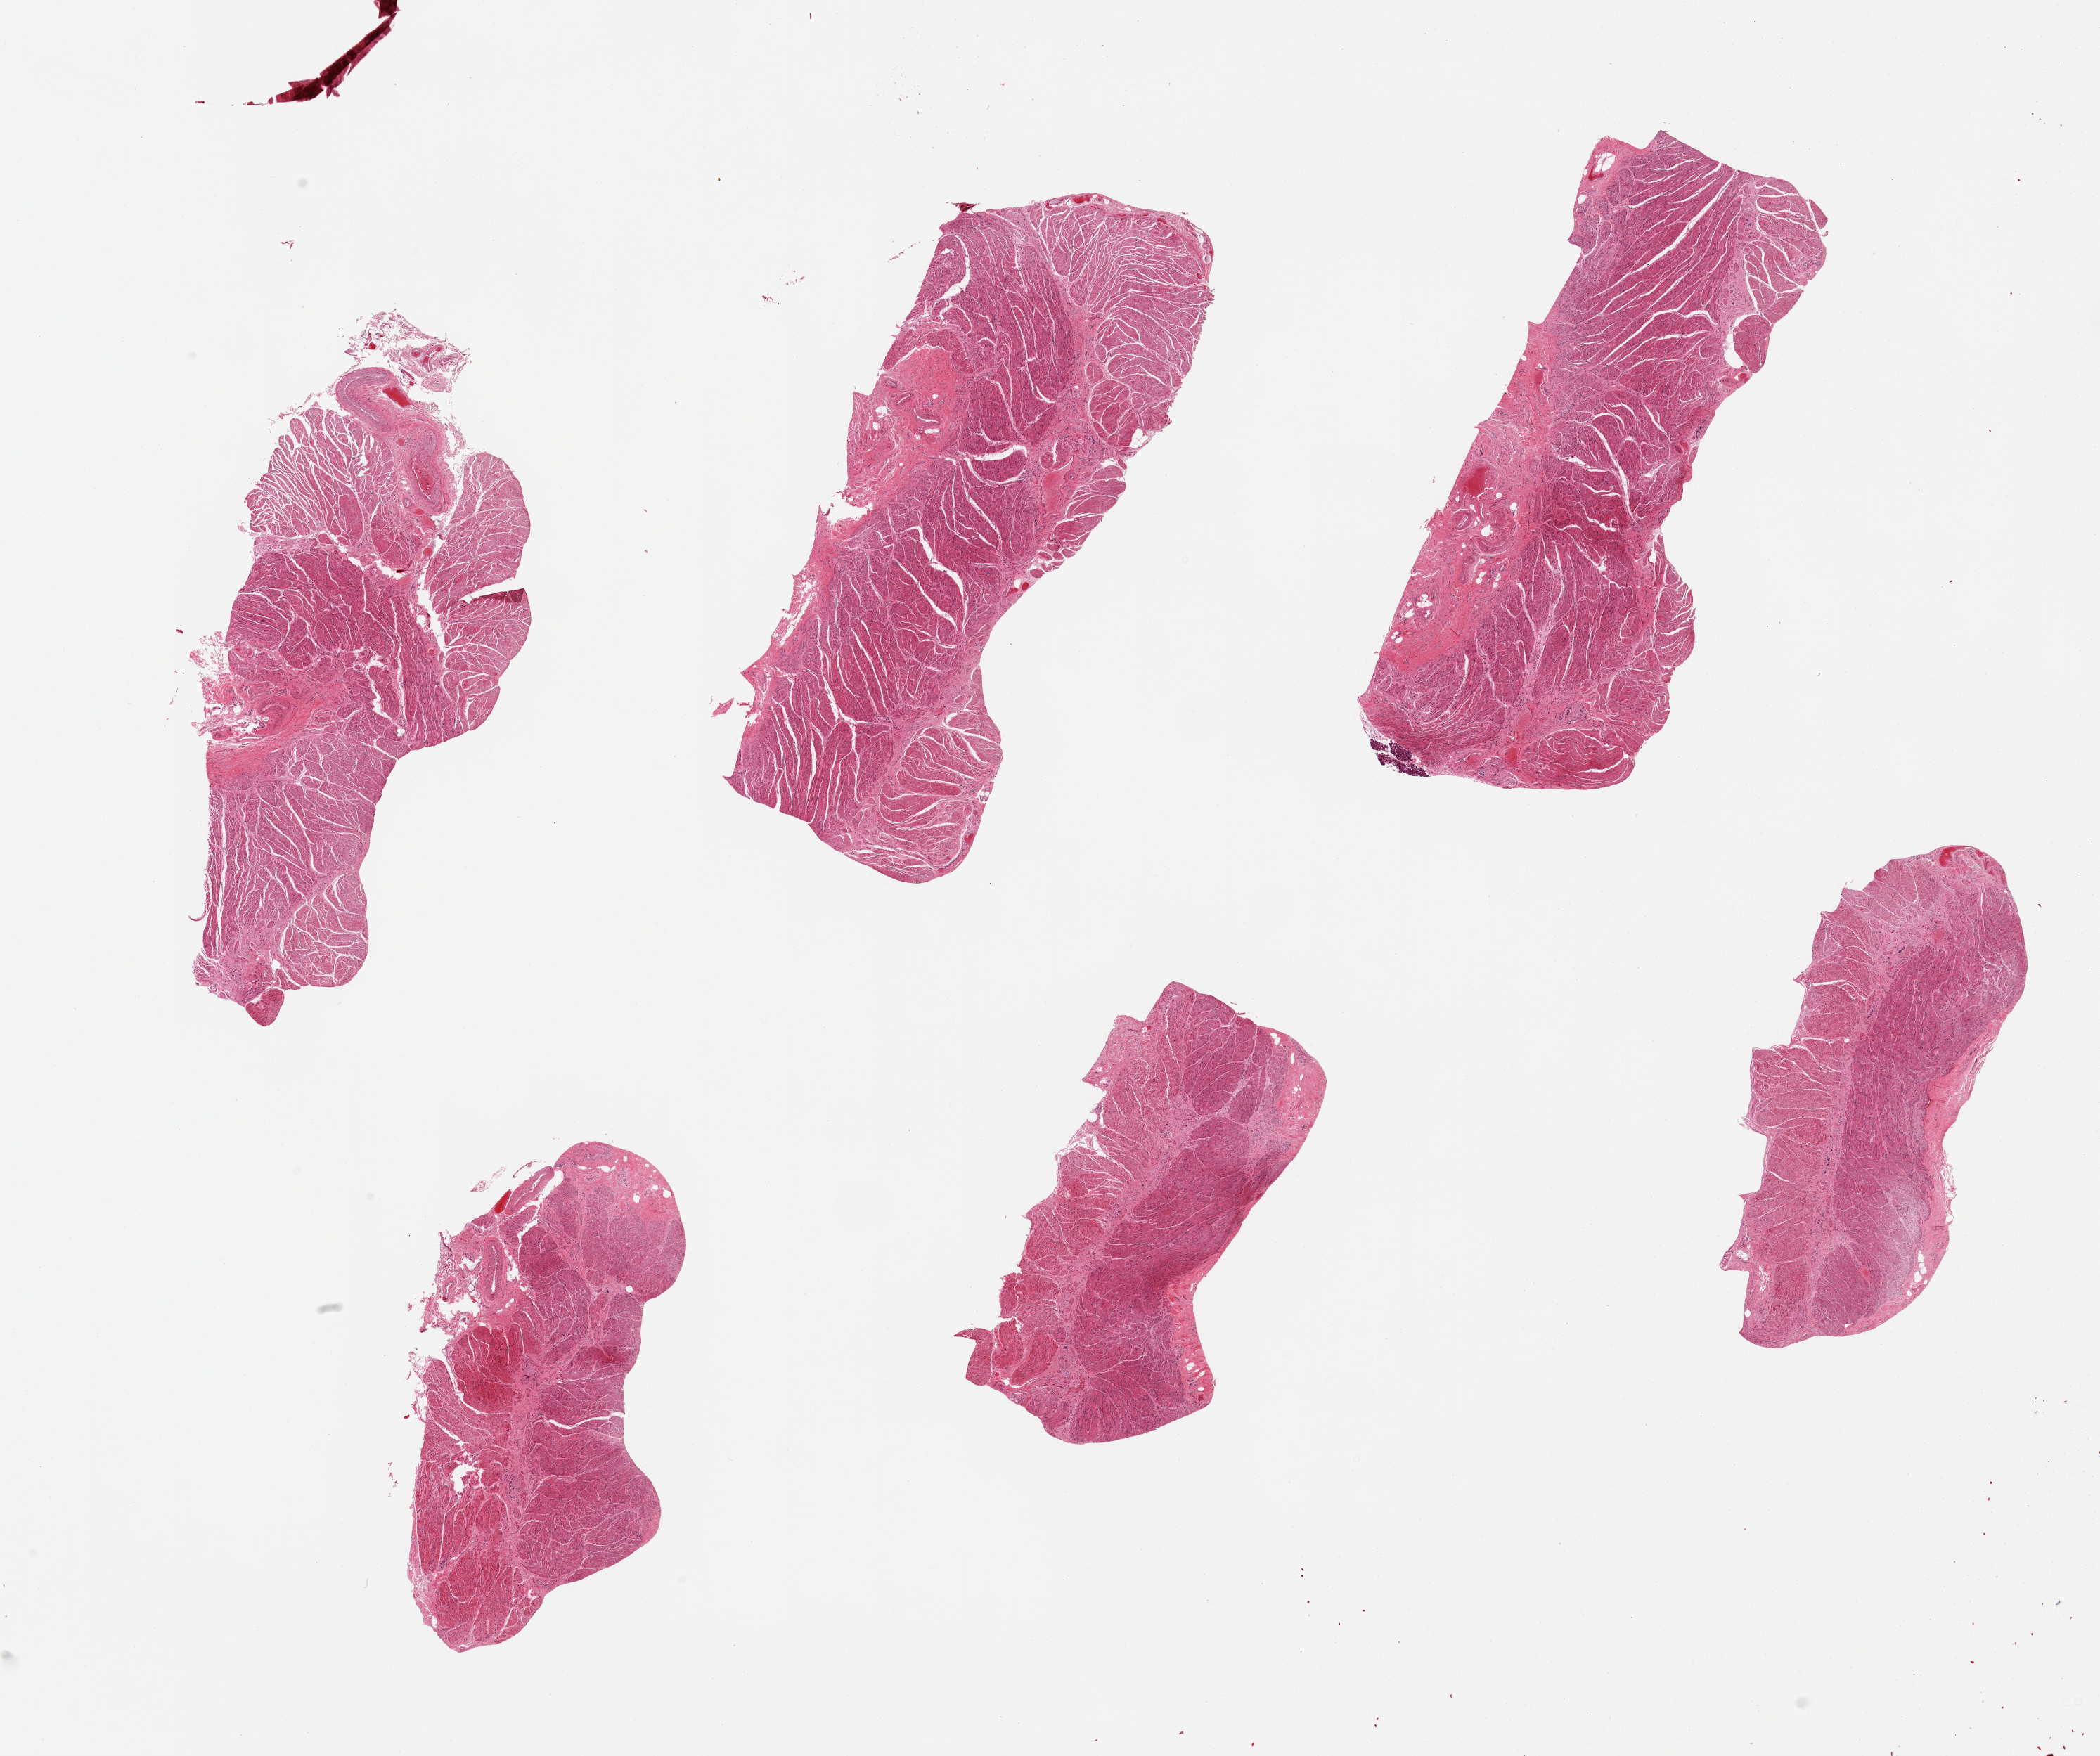
Whole-slide image, hematoxylin and eosin (H&E) stain, brightfield, whole scanned area (about 23.6 x 19.8 mm) shown as a low-resolution overview. PAXgene-fixed paraffin-embedded (PFPE) section. Target tissue: gastroesophageal junction. Tissue donor sample. Male donor.
Review note (as recorded): 6 pieces; well dissected.